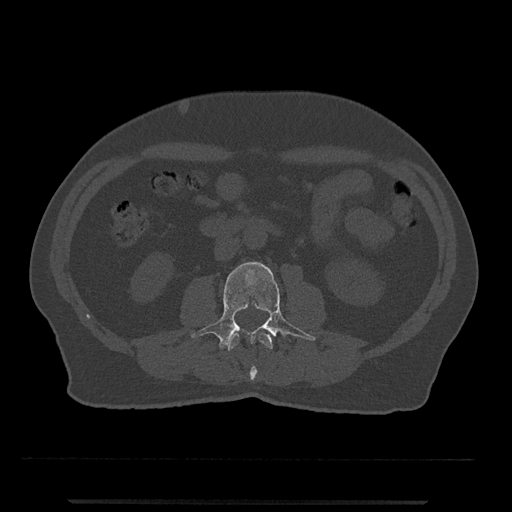
CT including the spine, one axial slice; position 212 of 797 along the scan axis; reconstruction kernel Br40s/3; 120 kVp; bone window (W 1800 / L 400 HU); 512 × 512 image matrix. Patient: male, 63 years. Case-level facts recorded for this patient, not image findings: primary cancer: prostate.
Outlined on this slice (semi-automatically segmented with operator editing):
- L2 vertebra: box from (x=227, y=333) to (x=273, y=381) px
- L3 vertebra: (x=191, y=262)–(x=316, y=349)